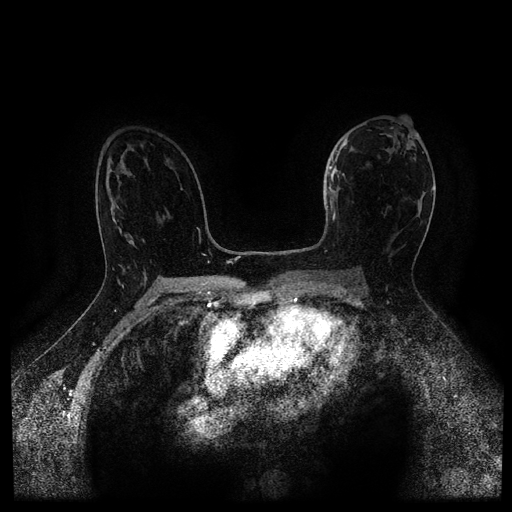
Breast MRI (dynamic contrast-enhanced, multi-phase), one axial slice. Position 61 of 116 along the scan axis. Dynamic contrast-enhanced series, time point 2 of 5 at this slice position (early post-contrast). 1.5 T. TE 2.7 ms, TR 5.4 ms. 2 mm slice thickness. 512 × 512 image matrix. Patient: female, 50 years.
Outlined on this slice (semi-automatic segmentation, software-assisted and operator-edited):
- breast lesion (labelled 'tumour' in the annotation; benign lesions carry a separate 'benign' label): bounding box [x1, y1, x2, y2] px = [328, 165, 339, 222]